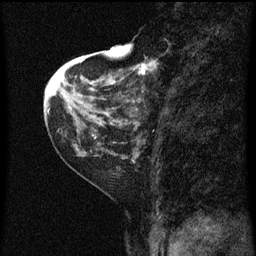
Breast MRI (dynamic contrast-enhanced), one sagittal slice. Slice 21 of 60 in the series (ordered by position). Dynamic contrast-enhanced series, image 2 of 3 at this slice position (ordered by acquisition). 1.5 T. TE 4.2 ms, TR 8 ms. 2 mm slice thickness. 256 × 256 image matrix. Patient: female, 48 years.
Annotated regions visible in this slice (semi-automatic segmentation, software-assisted and operator-edited):
- analysis volume of interest (the breast-tissue region the enhancement analysis was run in; not a lesion): bounding box (x1, y1, x2, y2) in pixels: (128, 54, 175, 125)
- tumour enhancement mask (voxels above the 70 % enhancement threshold inside the analysis volume of interest): (132, 58, 158, 125)